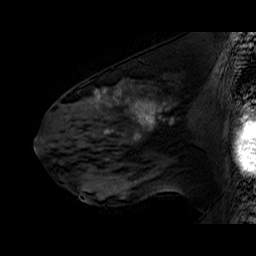
Breast MRI (dynamic contrast-enhanced), one sagittal slice. Slice 31 of 60 in the series (ordered by position). Dynamic contrast-enhanced series, time point 2 of 6 at this slice position (early post-contrast). 1.5 T. TE 6.4 ms, TR 32.9 ms. 4 mm slice thickness. 256 × 256 image matrix, field of view 200 × 200 mm. Female patient. Case-level facts recorded for this patient, not image findings: setting: breast cancer imaged before/during neoadjuvant chemotherapy; receptor status: HER2-positive.
Structures marked on this image (semi-automatic segmentation, software-assisted and operator-edited):
- analysis volume of interest (the breast-tissue region the enhancement analysis was run in; not a lesion): bounding box [x1, y1, x2, y2] px = [51, 78, 196, 160]
- tumour enhancement mask (voxels above the 100 % enhancement threshold inside the analysis volume of interest): [92, 88, 165, 131]